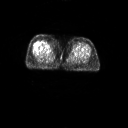
FDG PET of an extremity soft-tissue mass (from a PET/CT study), one axial slice. Slice 11 of 267 in the series (ordered by position). 3.27 mm slice thickness. 128 × 128 image matrix, field of view 700 × 700 mm. Female patient, age 56 years. From the clinical record (not read from this slice): histological type: malignant solitary fibrous tumor; grade: intermediate; site of the primary tumour: right thigh.
Outlined on this slice (expert contour drawn on MRI and transferred to this co-registered scan by the dataset authors):
- gross tumour volume including surrounding oedema: bounding box <42,41,51,47> (left, top, right, bottom; pixels)